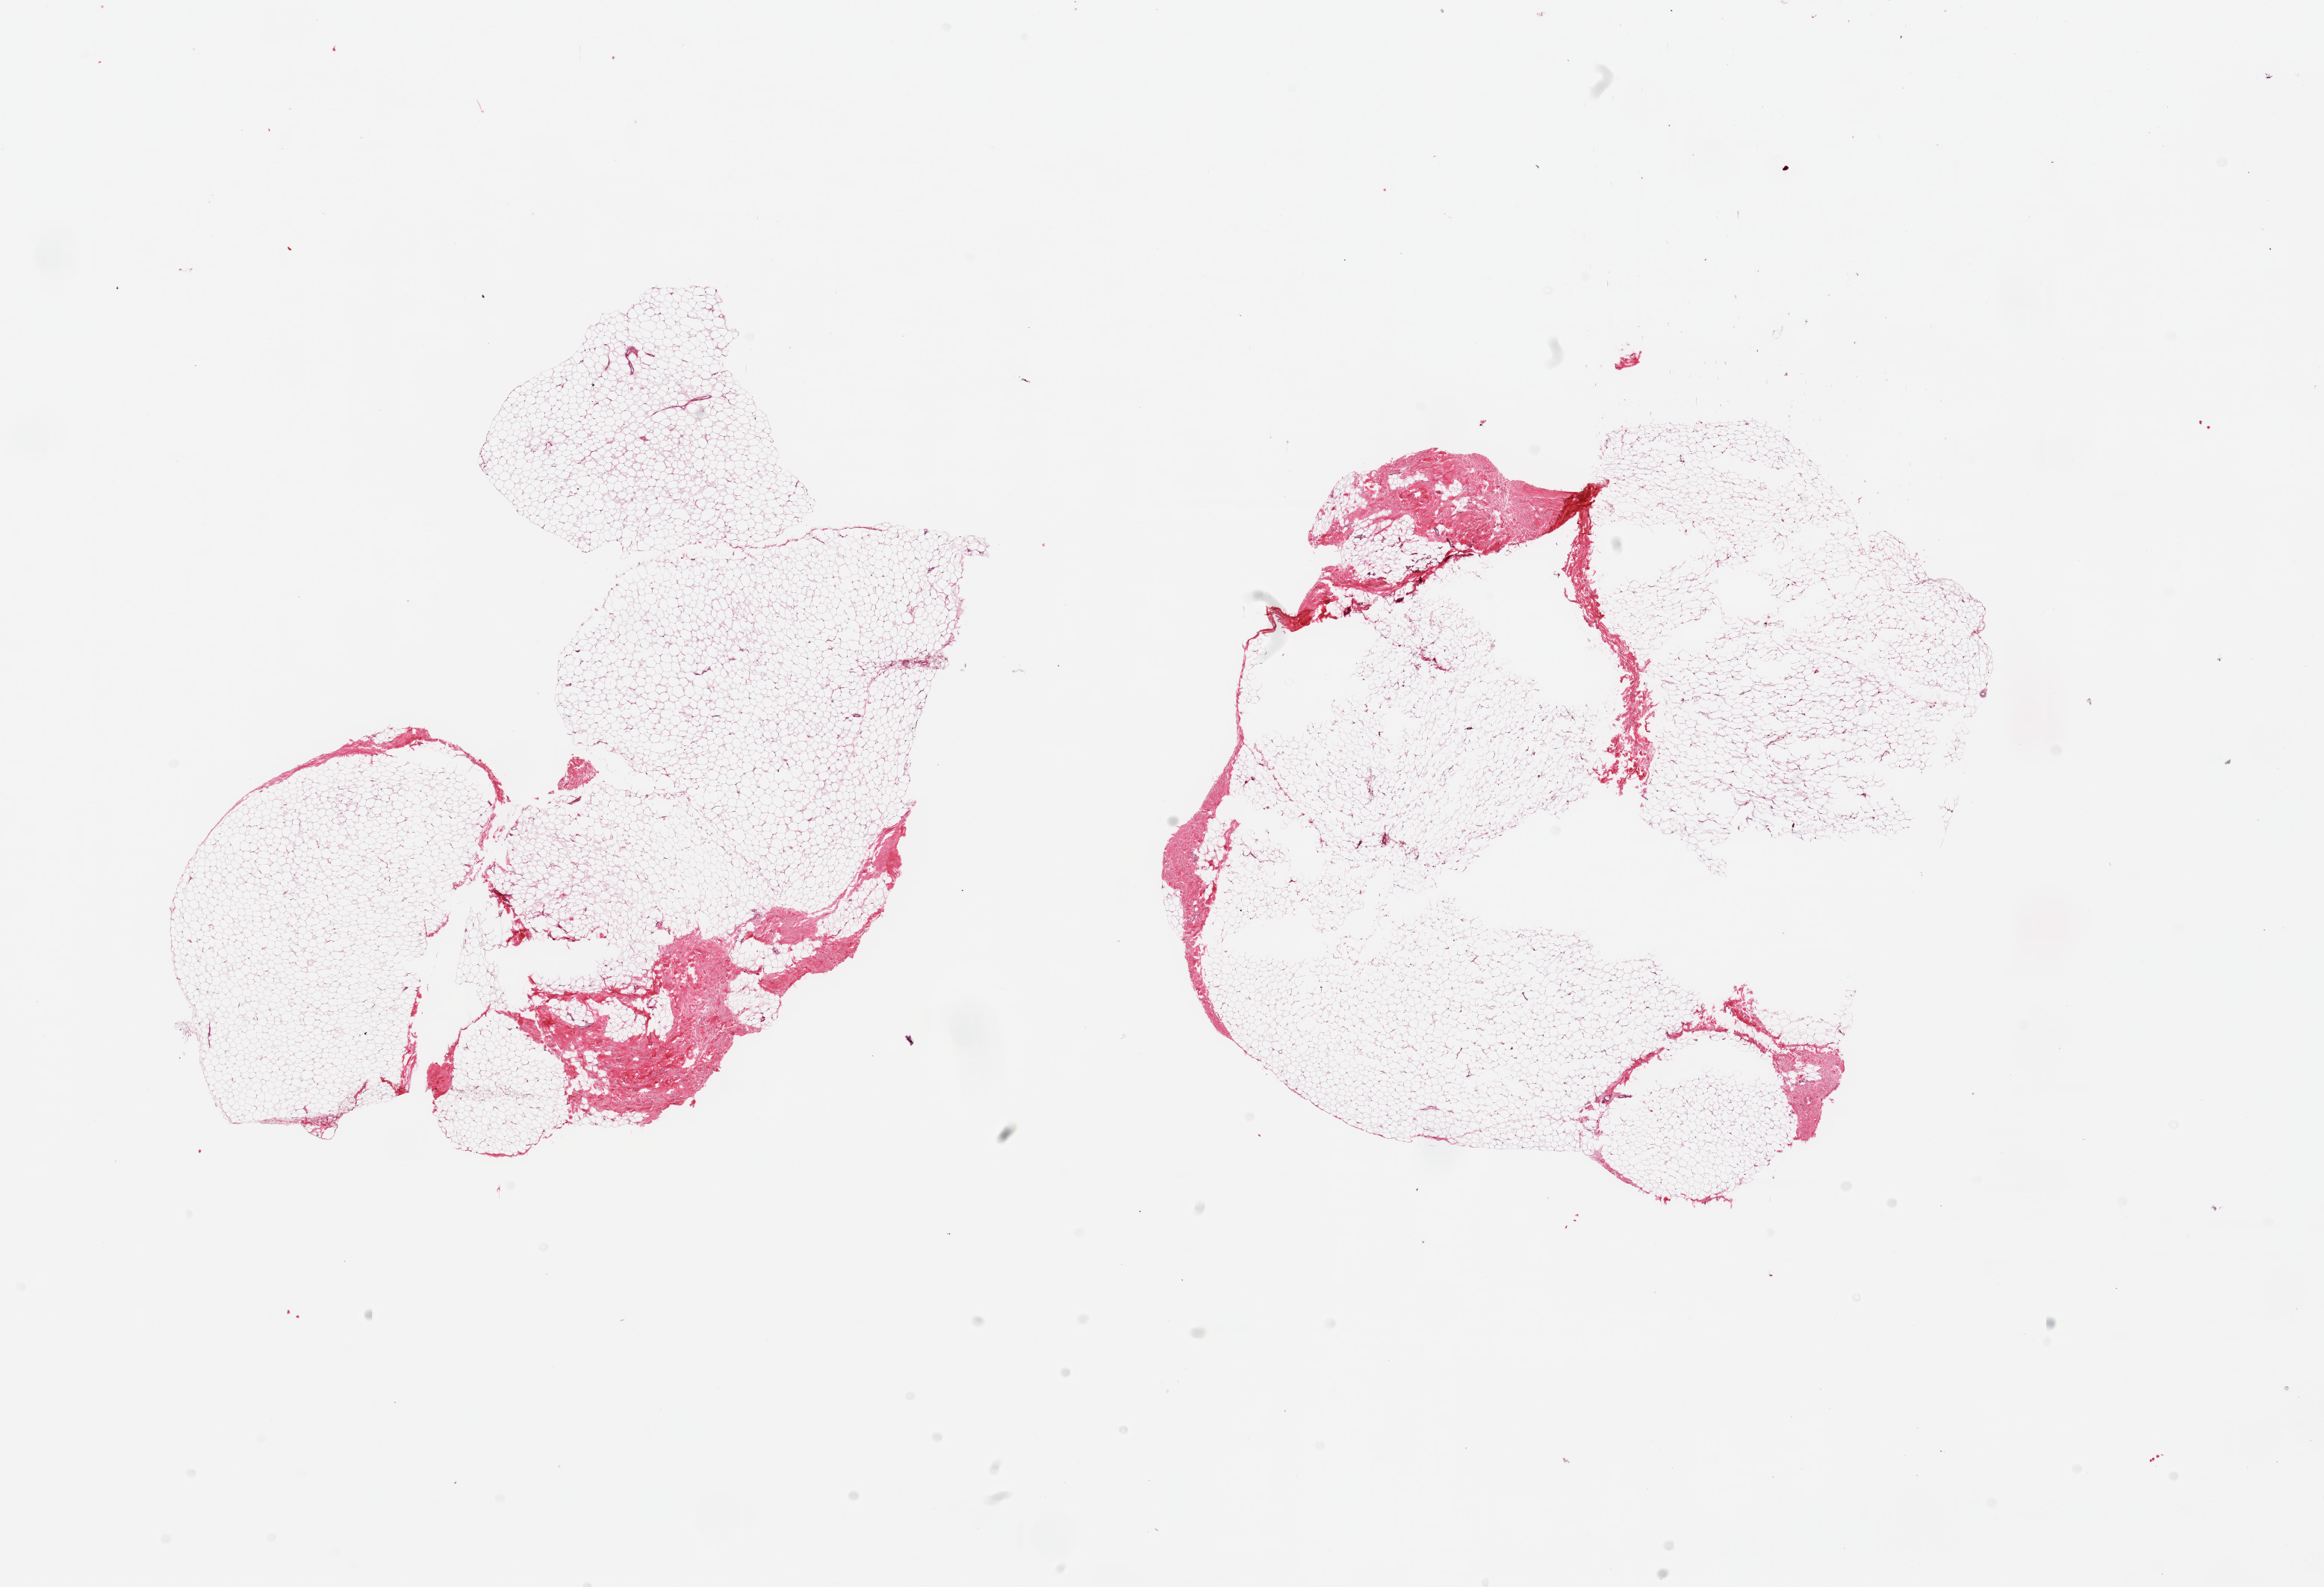
Haematoxylin and eosin whole-slide image — low-resolution overview of the scanned area, about 24.6 x 16.8 mm. PAXgene-fixed paraffin-embedded (PFPE) section. Sampled site (target tissue): breast. Donor tissue sample. Donor sex: male.
Review note (as recorded): 2 pieces; fibrofatty tissue without ducts.